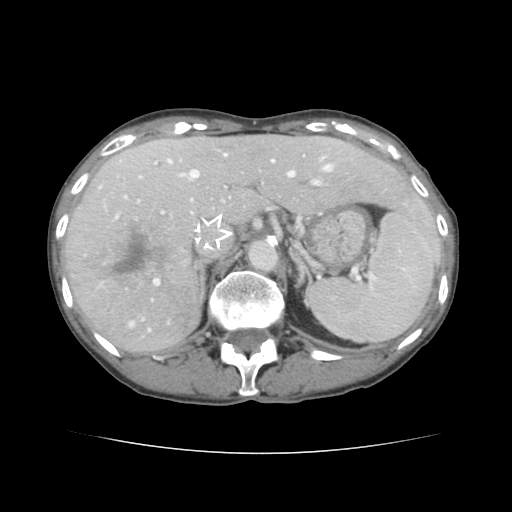
Contrast-enhanced abdominal CT, one axial slice; slice 97 of 136 in the series (ordered by position); 120 kVp; intravenous contrast given; soft-tissue window (W 400 / L 40 HU); 512 × 512 image matrix, field of view 319 × 319 mm. Female patient, age 77 years. Case-level facts recorded for this patient, not image findings: diagnosis: colorectal cancer liver metastases, imaged before liver resection; multiple liver metastases: yes; largest metastasis: 3 cm.
Annotated regions visible in this slice (outlined manually by an expert reader):
- hepatic veins: box from (x=129, y=153) to (x=332, y=331) px
- liver: (x=66, y=136)–(x=439, y=353)
- planned liver remnant (the part of the liver to remain after resection): (x=155, y=136)–(x=439, y=248)
- portal vein (with intrahepatic branches): (x=99, y=162)–(x=328, y=285)
- liver metastasis: (x=87, y=219)–(x=176, y=296)